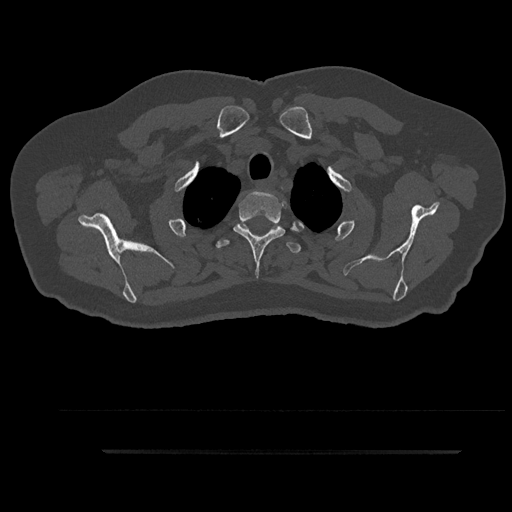
CT including the spine, one axial slice. Position 752 of 797 along the scan axis. Reconstruction kernel Br40s/3. 120 kVp. Bone window (W 1800 / L 400 HU). 0.5 mm slice thickness. 512 × 512 image matrix, field of view 432 × 432 mm. Patient: male, 63 years. Case-level facts recorded for this patient, not image findings: primary cancer: renal.
Annotated regions visible in this slice (semi-automatically segmented with operator editing):
- T2 vertebra: bounding box [x1, y1, x2, y2] px = [233, 191, 303, 277]
- T3 vertebra: [216, 222, 301, 254]